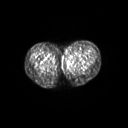
FDG PET of an extremity soft-tissue mass (from a PET/CT study), one axial slice. Slice 38 of 267 in the series (ordered by position). 3.27 mm slice thickness. 128 × 128 image matrix. Female patient, age 24 years. From the clinical record (not read from this slice): histological type: leiomyosarcoma; grade: high; site of the primary tumour: groin.
Annotated regions visible in this slice (expert contour drawn on MRI and transferred to this co-registered scan by the dataset authors):
- gross tumour volume including surrounding oedema: bounding box (x1, y1, x2, y2) in pixels: (61, 53, 72, 63)